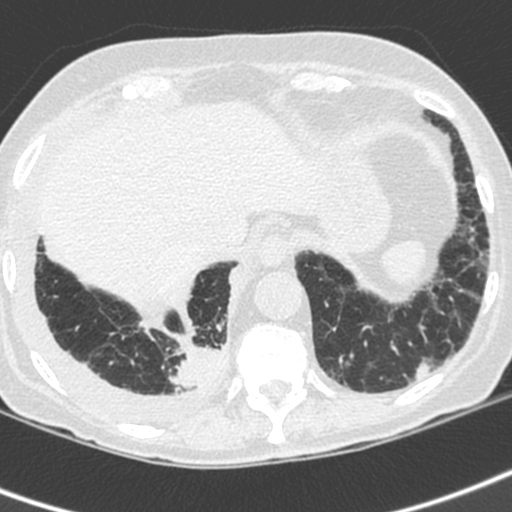
Low-dose screening chest CT, axial slice, first (baseline) screen, lung window (W 1500 / L -600 HU), 1.3 mm slice thickness, 512 × 512 image matrix. Female, age 73 years at enrolment. Current smoker at enrolment.
Lesion marked by an expert reader, box from (x=160, y=327) to (x=234, y=406) px. The exam's reader record, not a measurement of the box and not confirmed to be the same lesion: non-calcified nodule or mass ≥4 mm, right lower lobe, 35 × 30 mm, spiculated (stellate) margins, soft tissue attenuation. Later outcome: lung cancer diagnosed 22 days after this screen — adenocarcinoma, NOS, right lower lobe, stage IV (AJCC 6th edition), 35 mm at pathology.